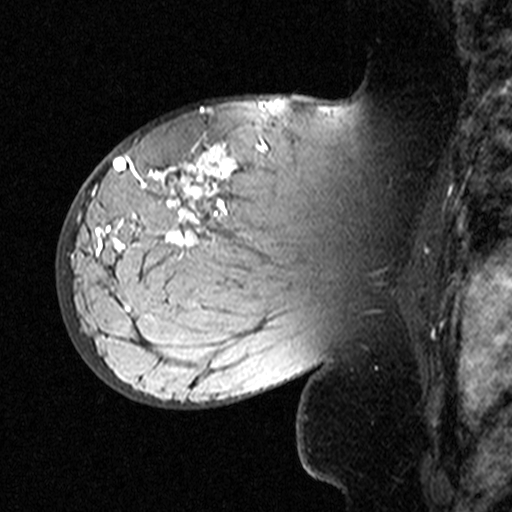
Breast MRI (dynamic contrast-enhanced), one sagittal slice; position 29 of 44 along the scan axis; dynamic contrast-enhanced study with each time point stored as its own series, time point 2 of 3 at this slice position (early post-contrast, ordered by acquisition time); 1.5 T; TE 4.5 ms, TR 11 ms; 3 mm slice thickness; 512 × 512 image matrix, field of view 200 × 200 mm. Patient: female, 53 years. Case-level facts recorded for this patient, not image findings: setting: breast cancer imaged before/during neoadjuvant chemotherapy; receptor status: HR-positive, HER2-negative.
Structures marked on this image (semi-automatically segmented with operator editing):
- analysis volume of interest (the breast-tissue region the enhancement analysis was run in; not a lesion): bounding box [x1, y1, x2, y2] px = [76, 140, 311, 353]
- tumour enhancement mask (voxels above the 90 % enhancement threshold inside the analysis volume of interest): [99, 143, 268, 253]